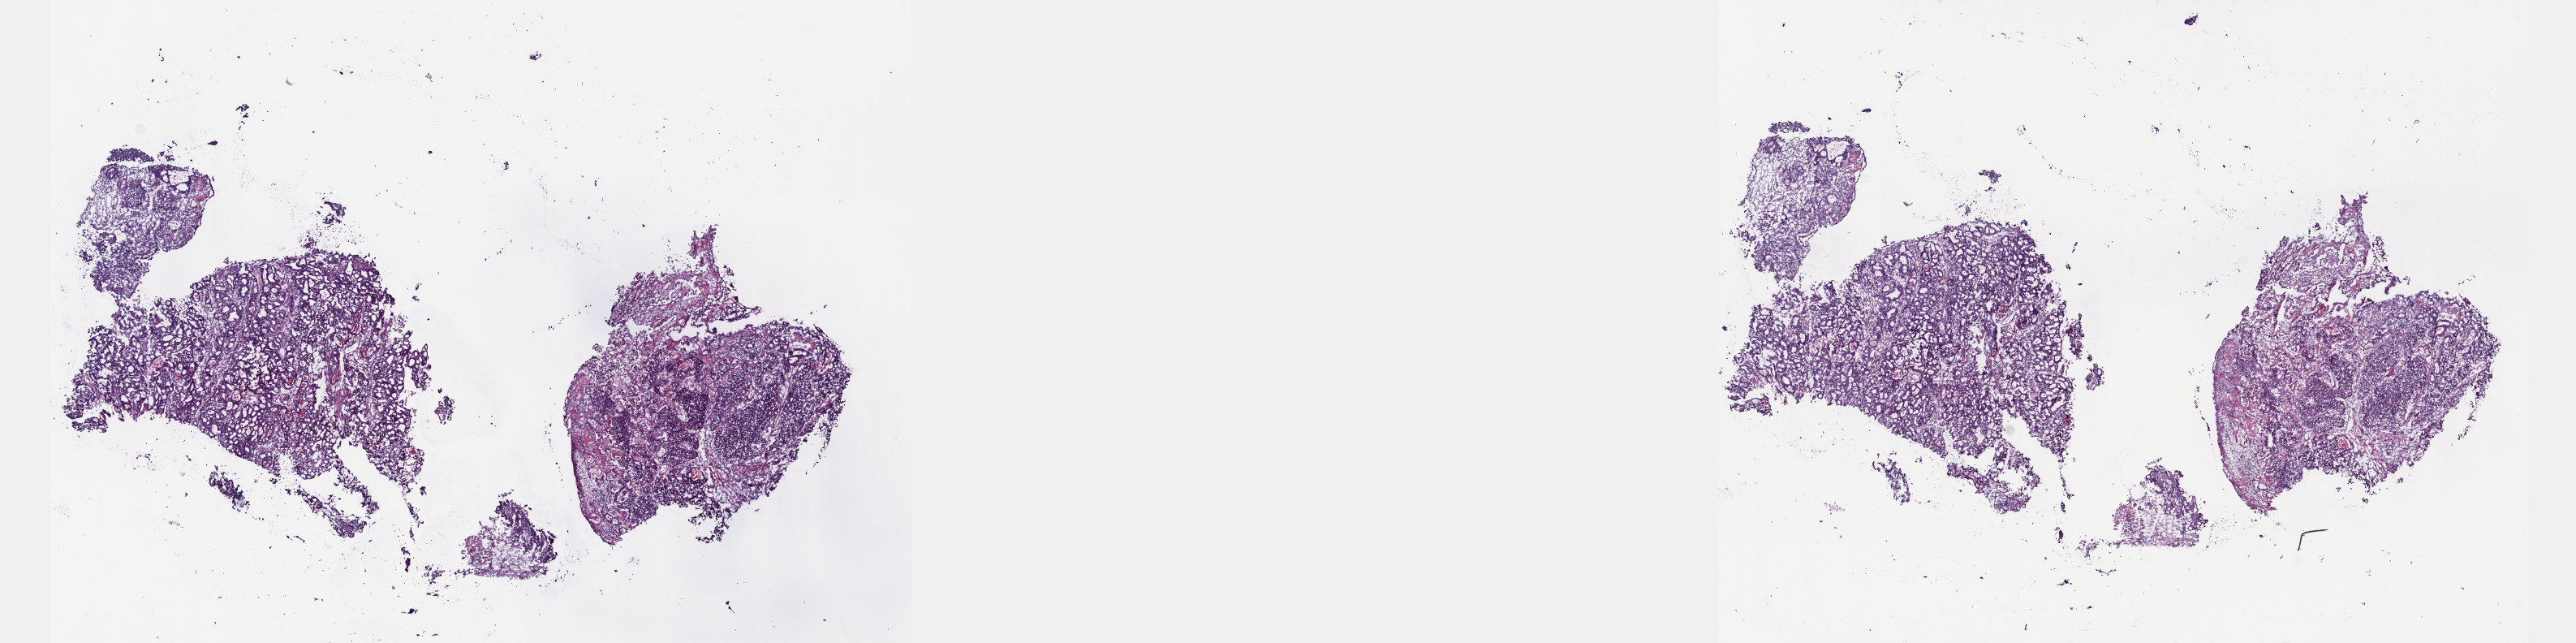
Whole-slide histology image, H&E — shown as a low-resolution overview of the whole scanned area (about 25.7 x 6.4 mm, slide scanned at 40x), frozen section from the top of the tissue portion, bile duct, primary tumour sample. Patient: female, age at initial diagnosis 72 years. Histologic grade: G3 (poorly differentiated). Slide review estimates, as recorded: tumour cells 60%, tumour nuclei 70%, normal cells 0%, stromal cells 40%, necrosis 0%. Infiltration values recorded for this section: lymphocyte infiltration 0%, monocyte infiltration 0%, neutrophil infiltration 0%.
• AJCC pathologic stage: I (7th edition)
• diagnosis: Cholangiocarcinoma